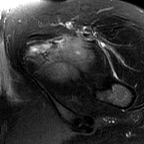
MRI of an extremity soft-tissue mass, one axial slice. Slice 49 of 60 in the series (ordered by position). T2-weighted fat-saturated. MR volume resampled by the dataset authors to the PET/CT grid (not the native acquisition matrix). 144 × 144 image matrix. Female patient. Case-level facts recorded for this patient, not image findings: histological type: pleiomorphic leiomyosarcoma; grade: intermediate; site of the primary tumour: left thigh.
Outlined on this slice (expert contour drawn on MRI and transferred to this co-registered scan by the dataset authors):
- gross tumour volume including surrounding oedema: bounding box <25,35,90,80> (left, top, right, bottom; pixels)
- gross tumour volume (mass): <47,40,87,79>